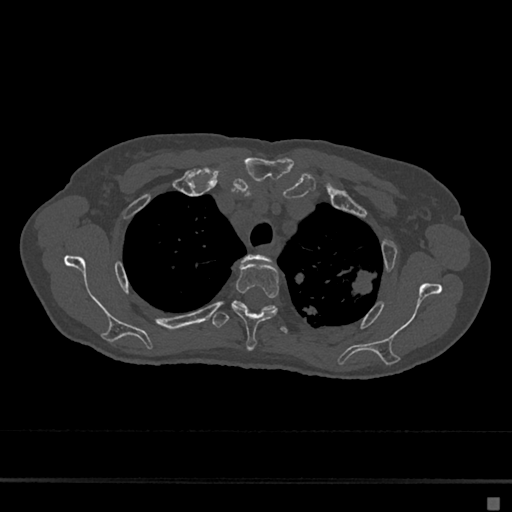
CT including the spine, one axial slice; position 532 of 797 along the scan axis; reconstruction kernel Br40s/3; 120 kVp; bone window (W 1800 / L 400 HU); 0.5 mm slice thickness; 512 × 512 image matrix, field of view 360 × 360 mm. Patient: female, 68 years. Case-level facts recorded for this patient, not image findings: primary cancer: renal.
Structures marked on this image (semi-automatically segmented with operator editing):
- T2 vertebra: box from (x=232, y=255) to (x=271, y=307) px
- T3 vertebra: (x=232, y=262)–(x=279, y=351)
- T4 vertebra: (x=212, y=304)–(x=288, y=334)